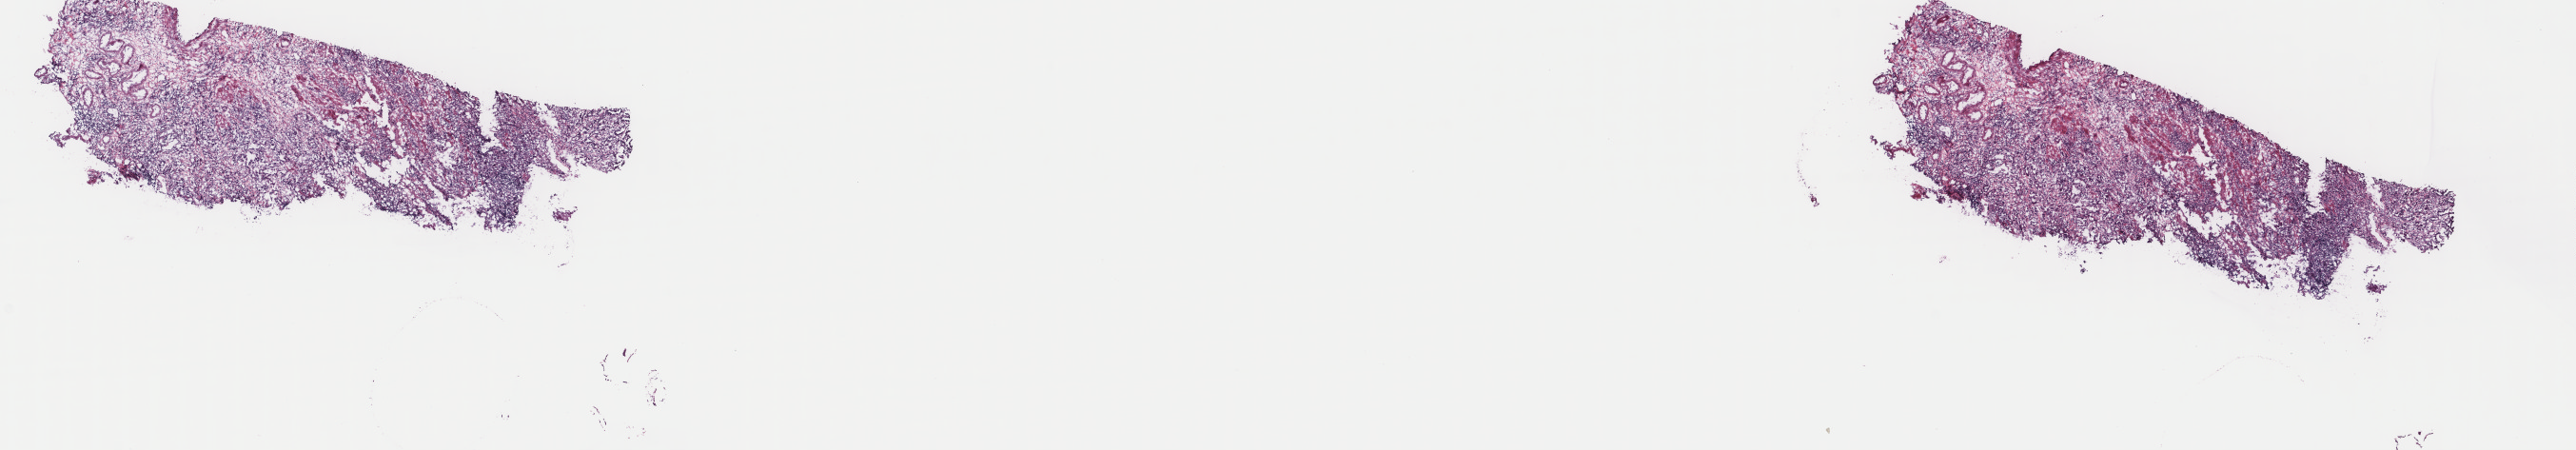
Digitized Hematoxylin and eosin (H&E) stained tissue section (whole slide), a low-resolution overview of the entire scanned area, about 21.5 x 3.8 mm (acquisition: 40x scan), frozen section from the top of the tissue portion, stomach, primary tumour sample. Male patient; age at initial diagnosis 64 years. Histologic grade: G3 (poorly differentiated). Pathologist review of this section (percent, as recorded): tumour cells 100%, tumour nuclei 70%, normal cells 0%, stromal cells 0%, necrosis 0%. Inflammatory infiltration, as recorded: lymphocyte infiltration 5%, monocyte infiltration 1%, neutrophil infiltration 1%.
AJCC pathologic stage: IA (7th edition). Histologic diagnosis: Adenocarcinoma, NOS. Lymph nodes positive (case pathology): 0 of 24 examined.